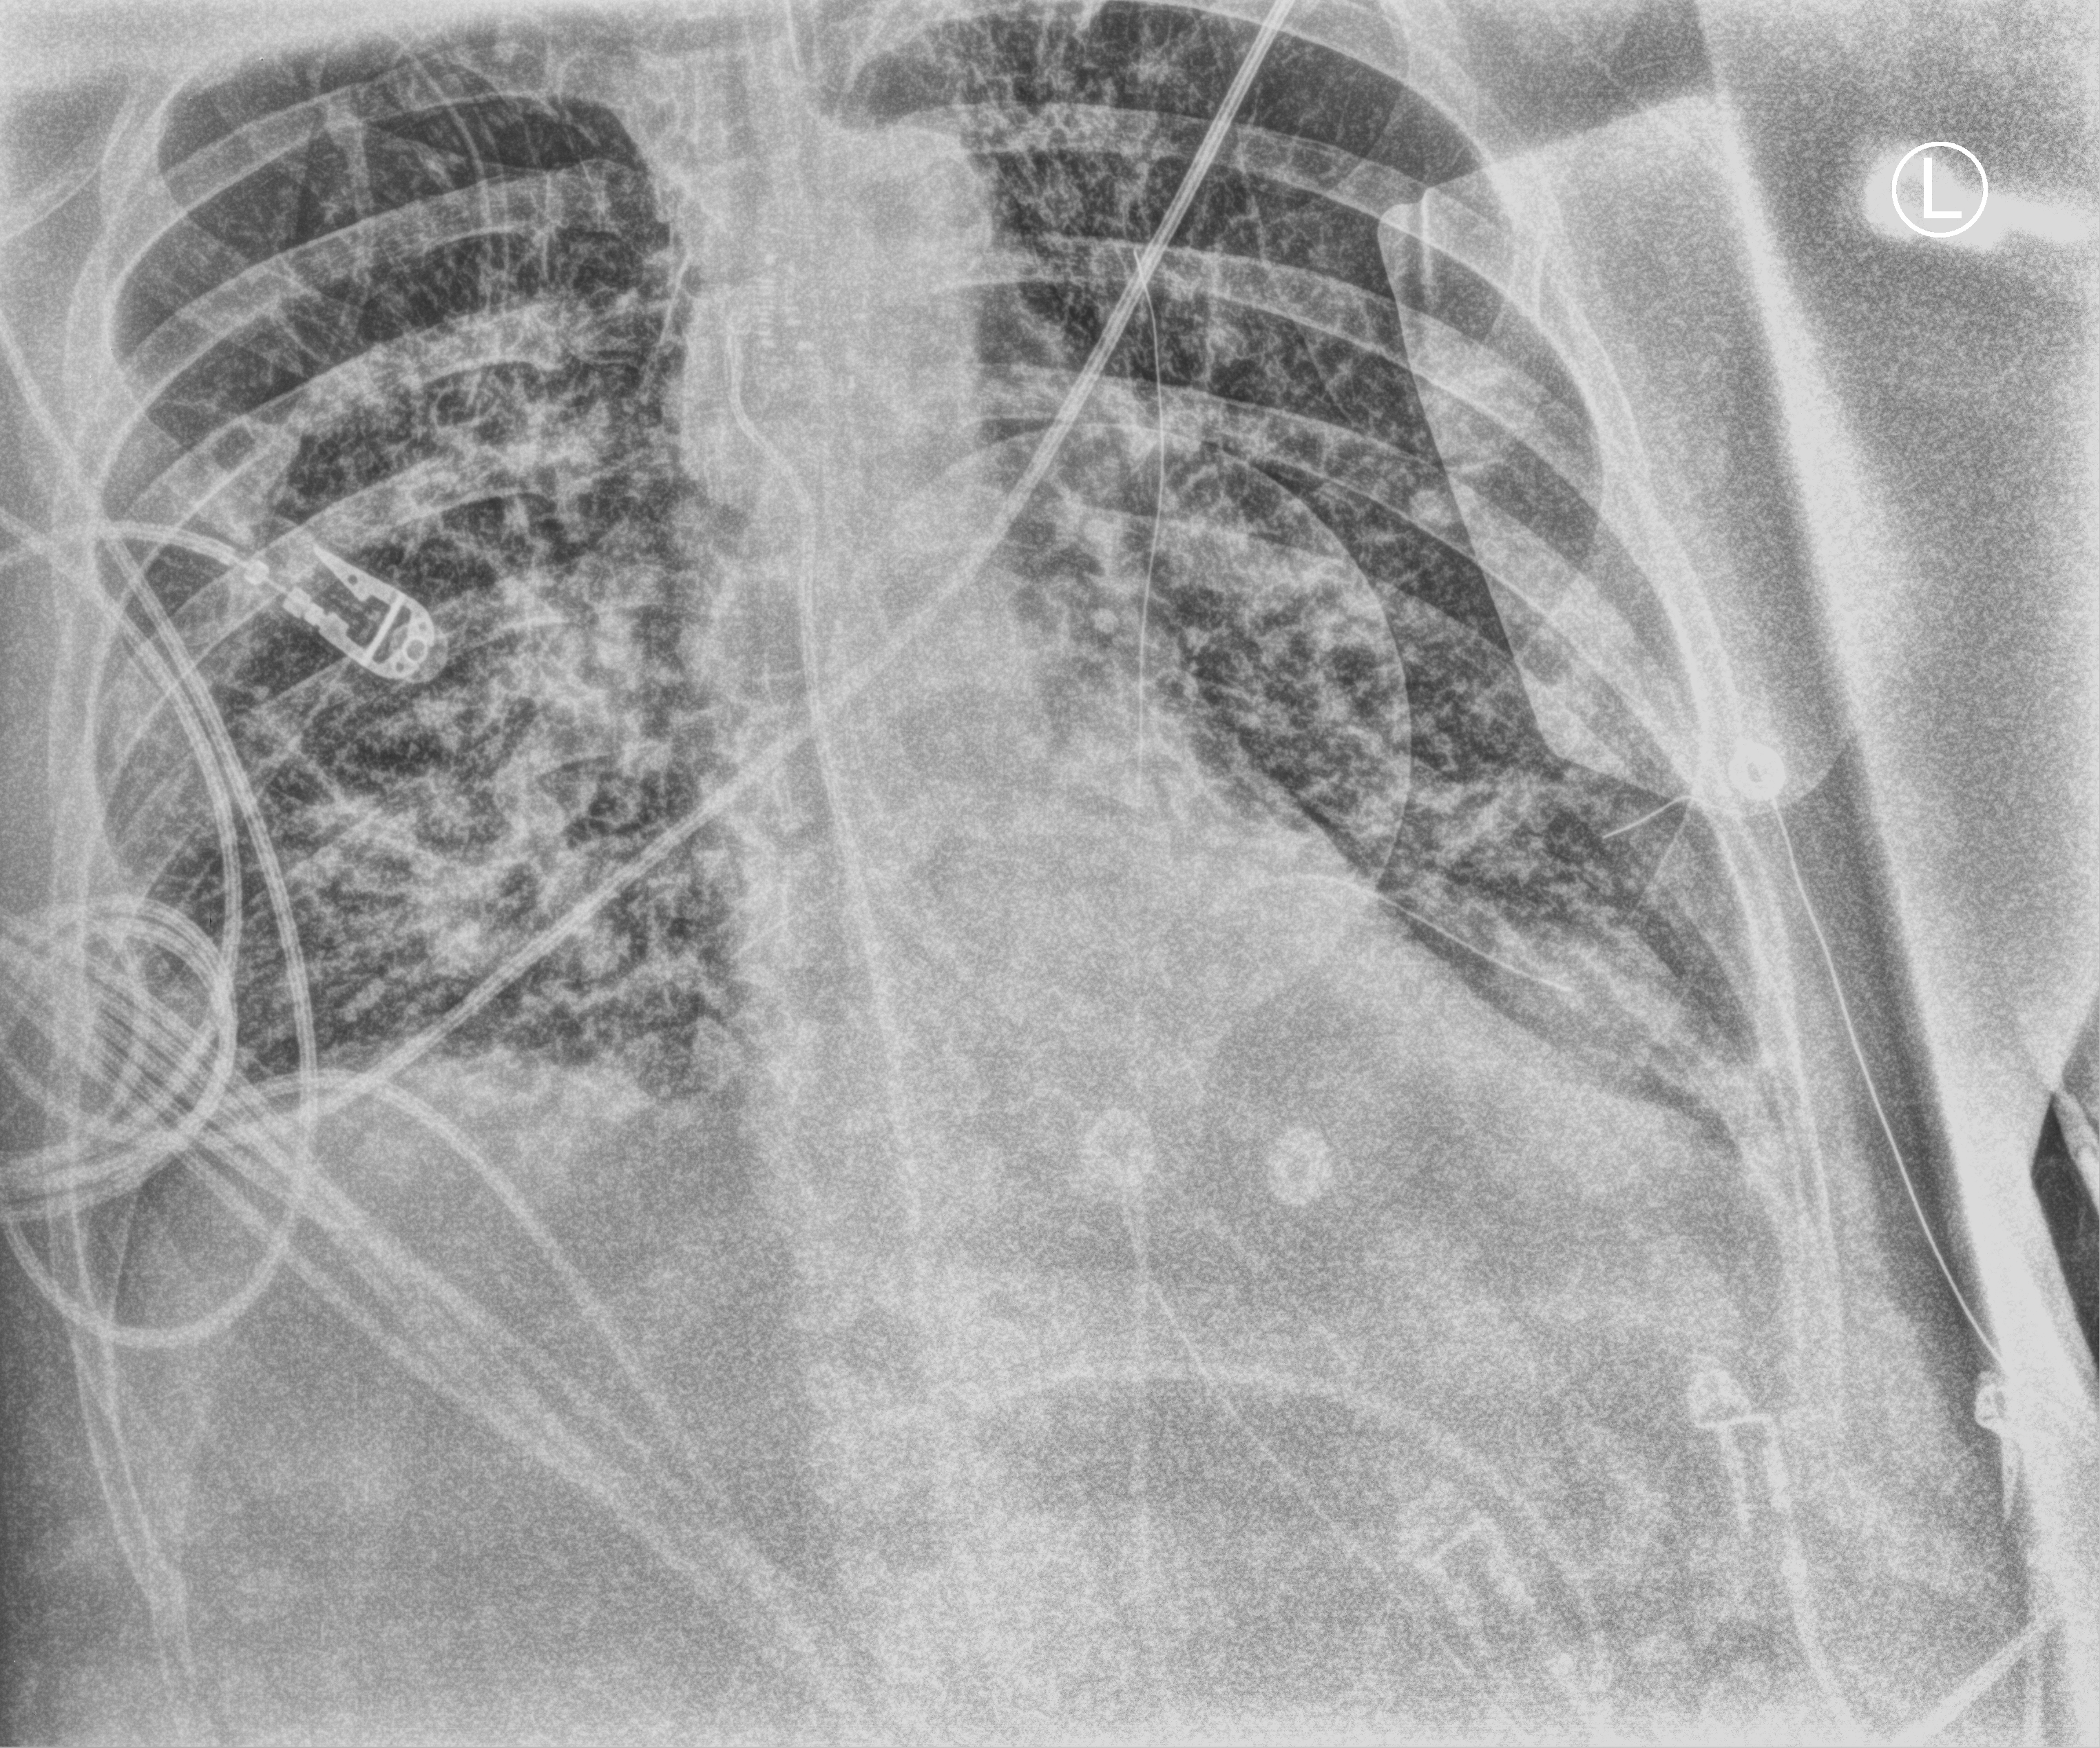
Chest X-ray (portable), anteroposterior (AP) projection. Patient hospitalised with COVID-19, aged 18–59 years.
Hospital-stay facts (about this admission, not read from this image; timing relative to this image not recorded):
- mechanically ventilated during this hospital stay: yes
- admitted to intensive care during this hospital stay: yes